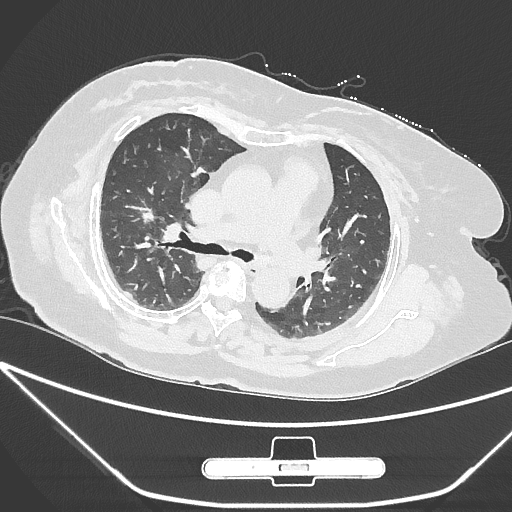
Chest CT, one axial slice; slice 166 of 245 in the series (ordered by position); reconstruction kernel IMR1,SharpPlus; lung window (W 1500 / L -600 HU); 512 × 512 image matrix. Female patient, age 65 years. Case-level facts recorded for this patient, not image findings: clinical TNM (as recorded): T1c N0 M0.
Annotated regions visible in this slice (bounding box drawn by a radiologist):
- lung tumour (recorded histology: adenocarcinoma): bounding box <131,203,160,236> (left, top, right, bottom; pixels)